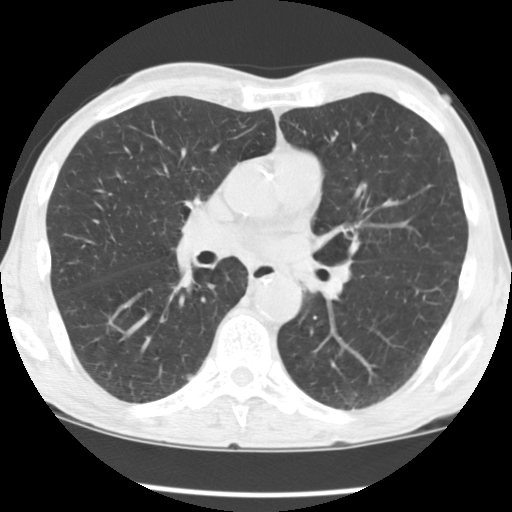
Chest CT (low-dose screening protocol), one axial image; baseline screening round; lung window (W 1500 / L -600 HU); 2.5 mm slice thickness; standard (soft-tissue) reconstruction kernel (STANDARD); slice 66 of 135 in the series. Male participant, aged 68 years at enrolment. Current smoker at enrolment.
Lesion marked by an expert reader, bounding box (x1, y1, x2, y2) in pixels: (174, 360, 208, 395). The screening reader recorded 4 non-calcified nodules or masses ≥4 mm on this exam (right middle lobe, left upper lobe, right lower lobe, right lower lobe); which of them this box marks is not recorded. Participant outcome: lung cancer diagnosed 284 days after this screen — adenocarcinoma, NOS, right lower lobe, moderately differentiated (G2), stage IV (AJCC 6th edition), 14 mm at pathology.